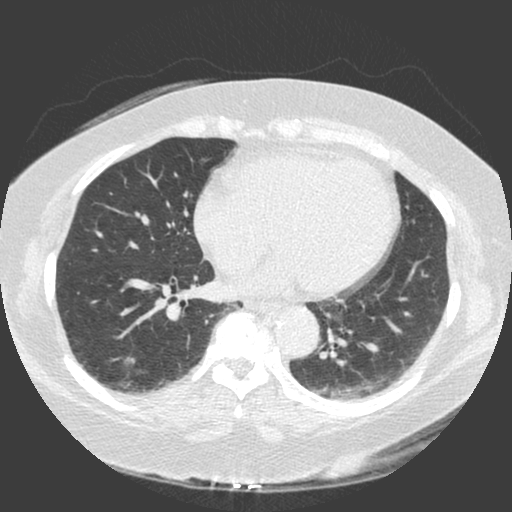
Axial slice from a low-dose chest CT screening exam. Second screening round (one year after baseline). Lung window (W 1500 / L -600 HU). 2 mm slice thickness. 120 kVp. Slice 100 of 175 in the series. Female participant, aged 56 years at enrolment. Current smoker at enrolment.
- Expert reader's lesion annotation, bounding box <110,343,146,380> (left, top, right, bottom; pixels).
- No non-calcified nodule or mass ≥4 mm was recorded by the screening reader at this exam.
- Official screen result: negative screen, no significant abnormalities.
- Participant outcome: lung cancer diagnosed 440 days after this screen (after the third annual screen) — adenosquamous carcinoma, right lower lobe, poorly differentiated (G3), stage IA (AJCC 6th edition), 25 mm at pathology.